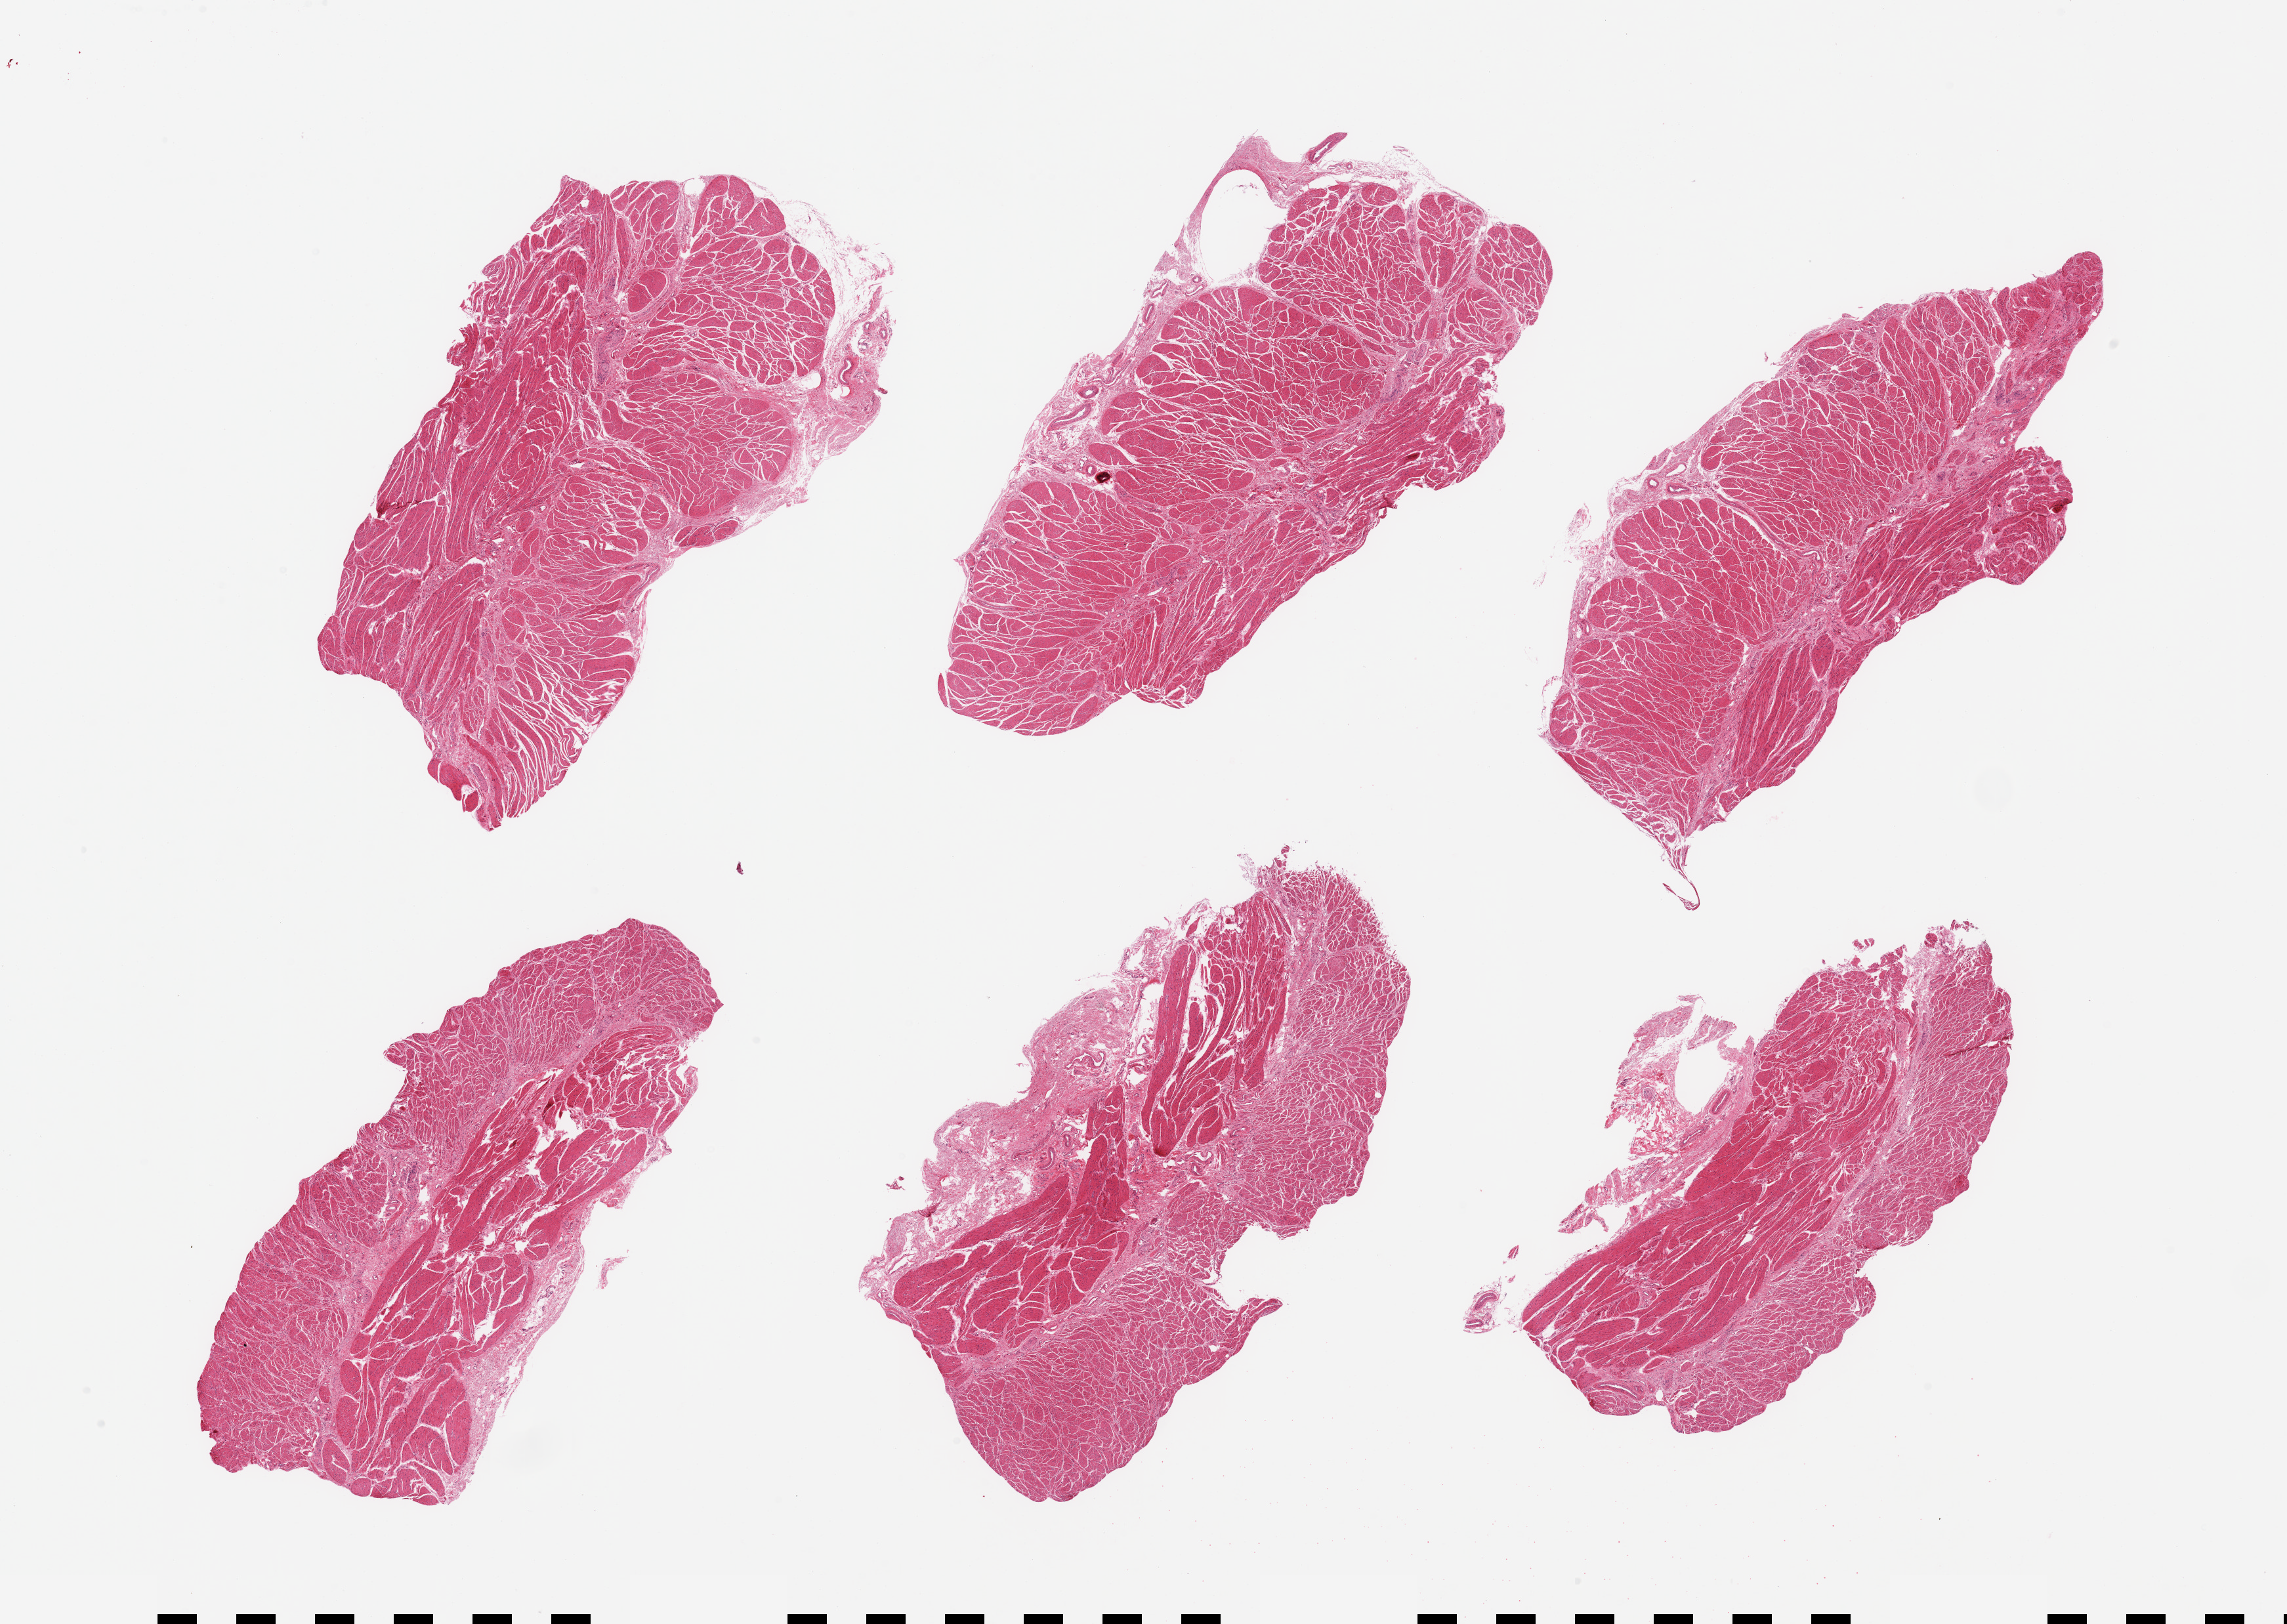
Digitized haematoxylin and eosin-stained section, low-resolution overview of the scanned area, about 27.6 x 19.6 mm; PAXgene-fixed, paraffin-embedded tissue; section of gastroesophageal junction (target tissue); tissue donor sample. Donor sex: male.
Pathologist's review note for this sample: 6 pieces, confirmed target muscularis.